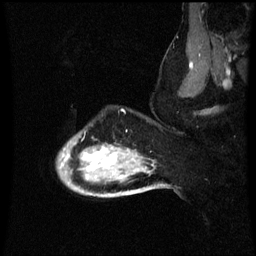
Breast MRI (dynamic contrast-enhanced), one sagittal slice. Slice 51 of 60 in the series (ordered by position). Dynamic contrast-enhanced series, image 2 of 3 at this slice position (ordered by acquisition). 1.5 T. TE 4.2 ms, TR 8.9 ms. 2 mm slice thickness. 256 × 256 image matrix. Female patient, age 49 years. From the clinical record (not read from this slice): setting: breast cancer imaged before/during neoadjuvant chemotherapy; receptor status: HR-positive, HER2-negative.
Annotated regions visible in this slice (semi-automatic segmentation, software-assisted and operator-edited):
- analysis volume of interest (the breast-tissue region the enhancement analysis was run in; not a lesion): bounding box <58,132,159,199> (left, top, right, bottom; pixels)
- tumour enhancement mask (voxels above the 70 % enhancement threshold inside the analysis volume of interest): <68,144,137,171>